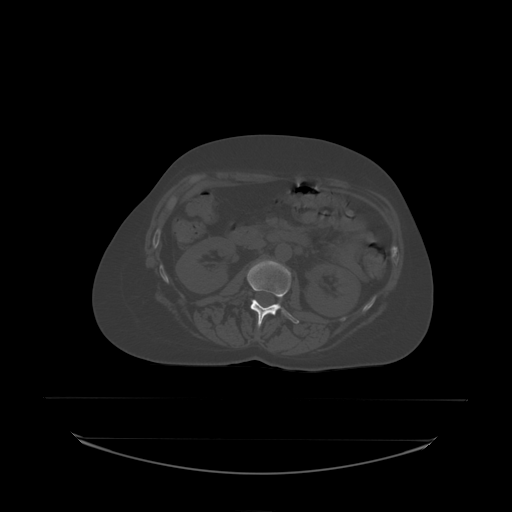
CT including the spine, one axial slice; slice 71 of 242 in the series (ordered by position); bone window (W 1800 / L 400 HU); 512 × 512 image matrix, field of view 500 × 500 mm. Female patient, age 53 years. From the clinical record (not read from this slice): primary cancer: lung.
Outlined on this slice (semi-automatic segmentation, software-assisted and operator-edited):
- L2 vertebra: box from (x=247, y=260) to (x=300, y=328) px